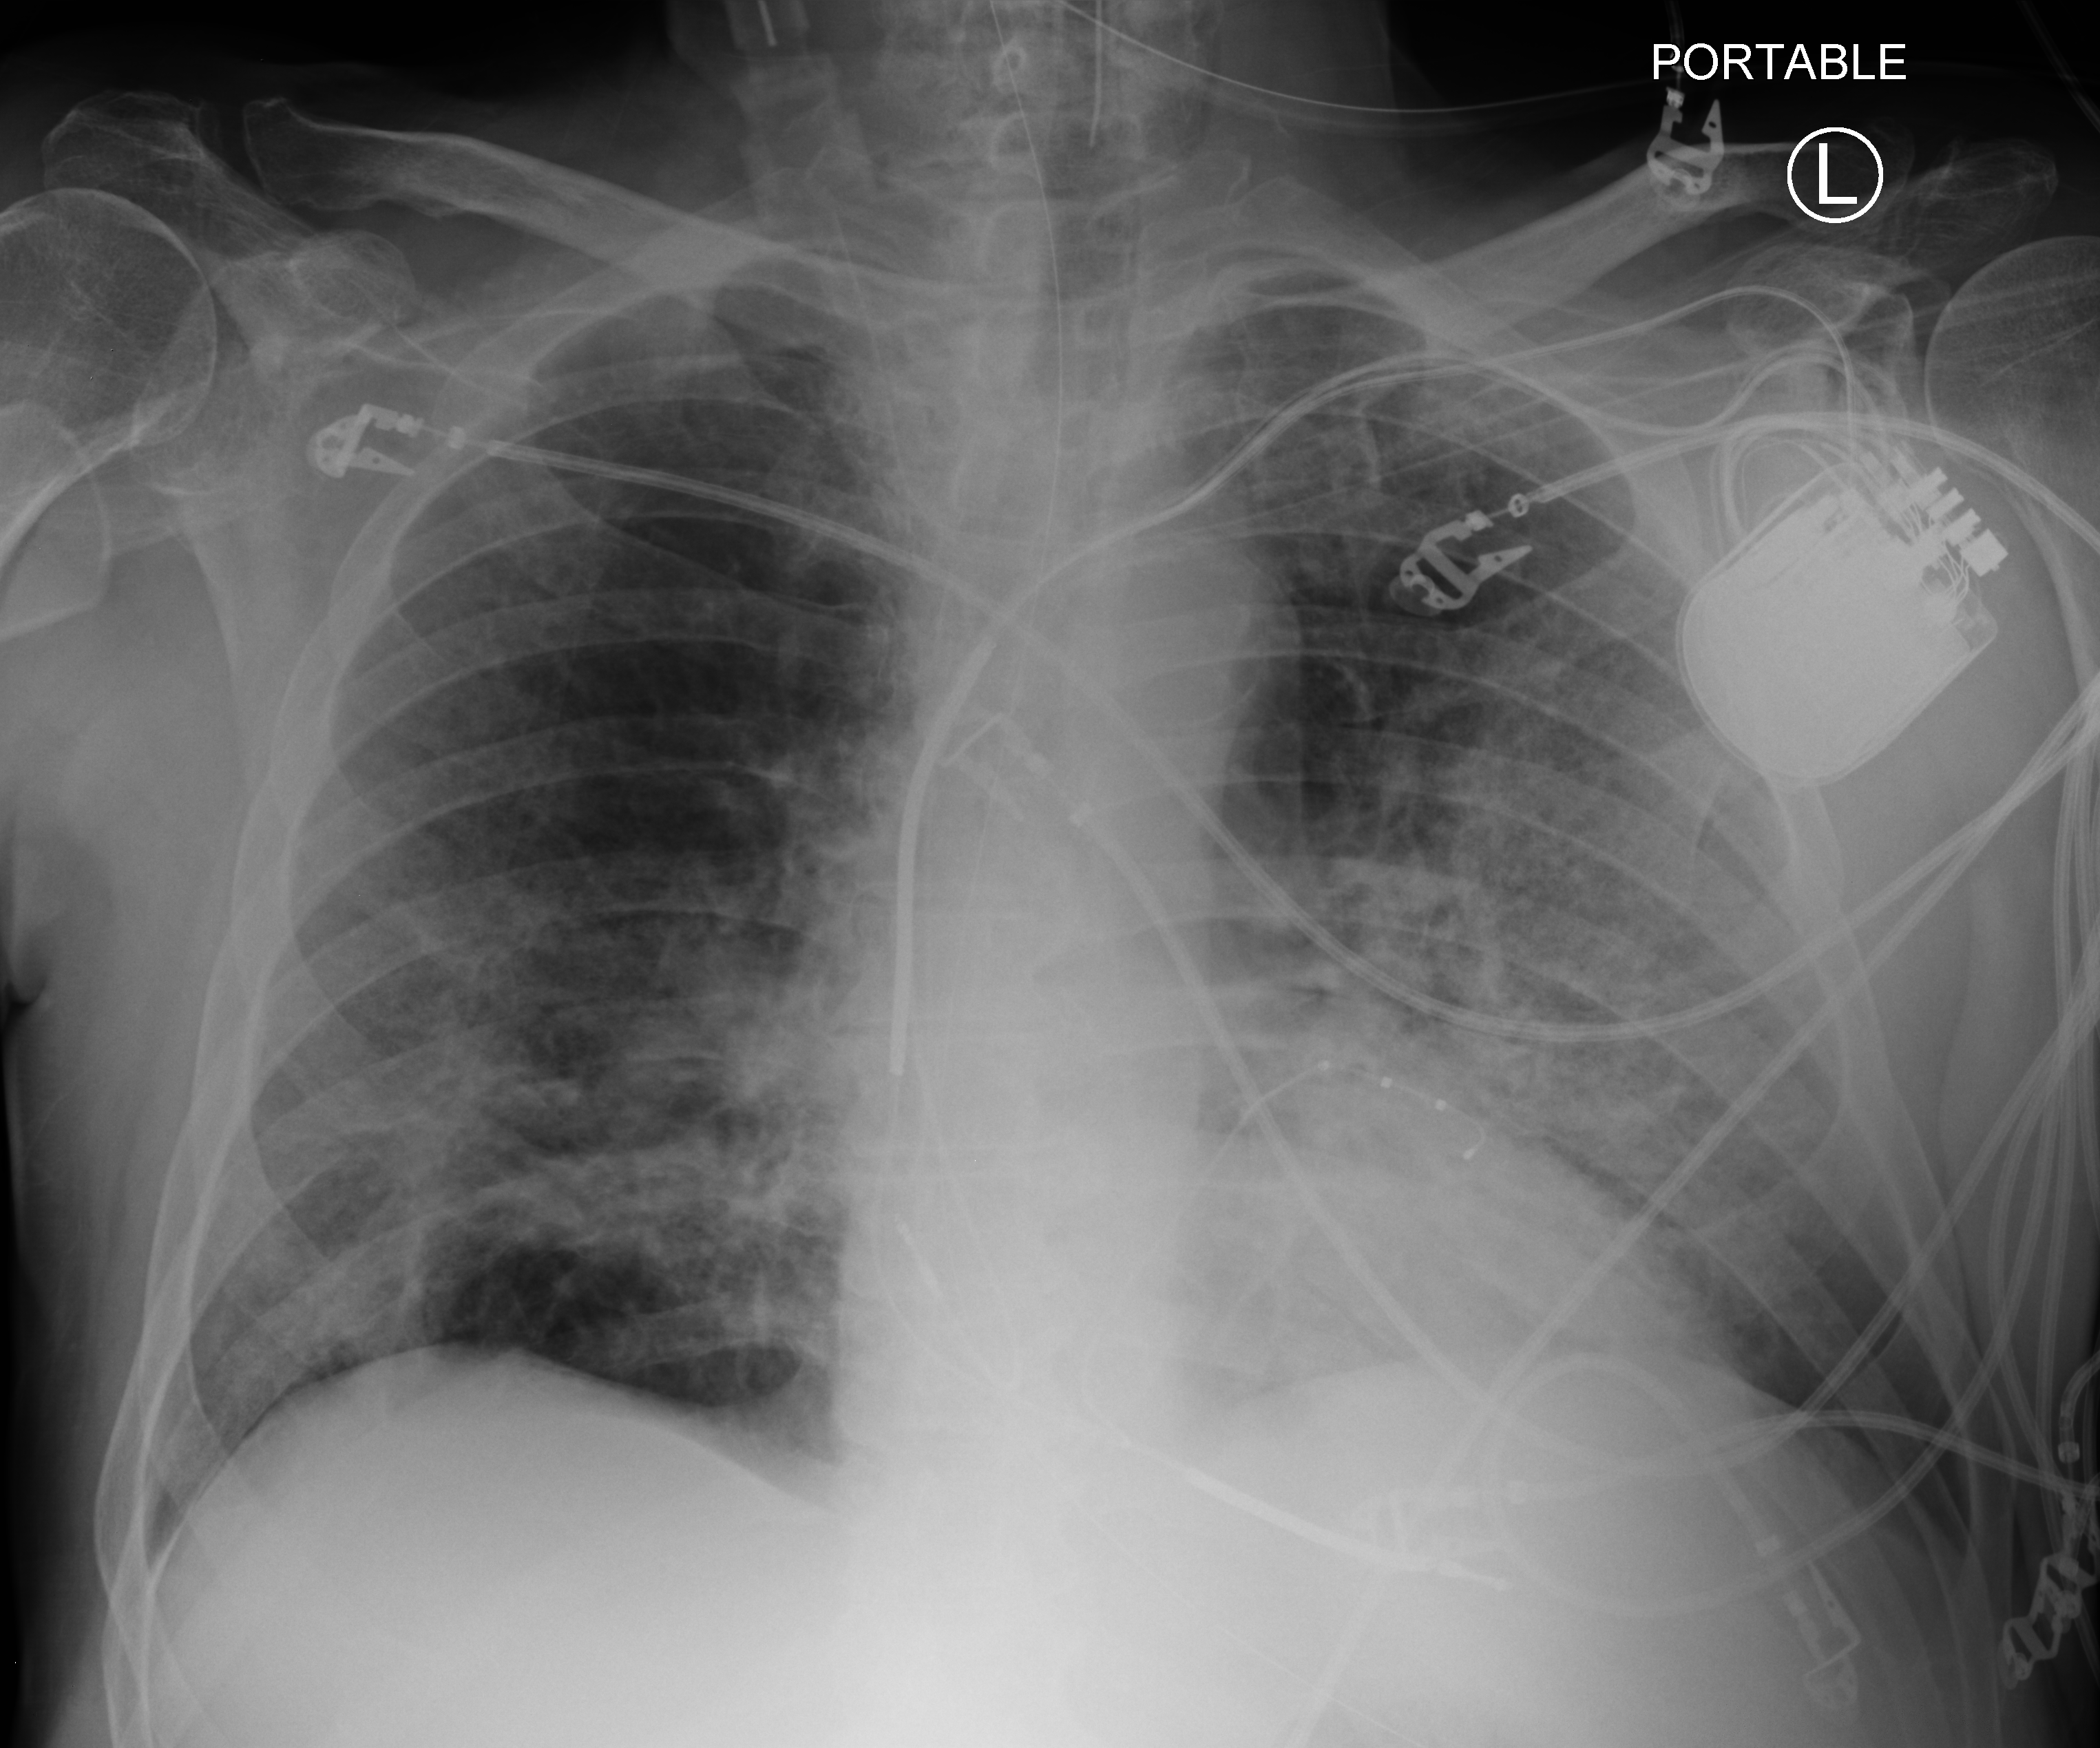
Chest X-ray (portable), anteroposterior (AP) projection. Patient hospitalised with COVID-19; male, aged 60–74 years.
From the hospital-stay record, not from the radiograph (when in the stay this image was taken is not recorded):
- length of hospital stay: 36 days
- diabetes (admission record): yes